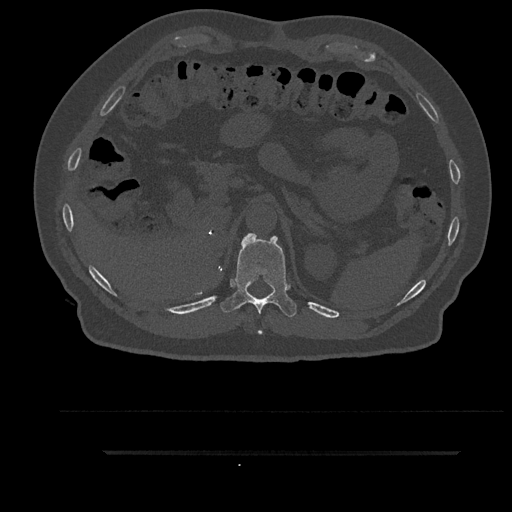
CT including the spine, one axial slice. Position 306 of 797 along the scan axis. Reconstruction kernel Br40s/3. Bone window (W 1800 / L 400 HU). 512 × 512 image matrix, field of view 432 × 432 mm. Male patient, age 63 years. From the clinical record (not read from this slice): primary cancer: renal.
Annotated regions visible in this slice (semi-automatically segmented with operator editing):
- T11 vertebra: bounding box [x1, y1, x2, y2] px = [220, 233, 297, 335]